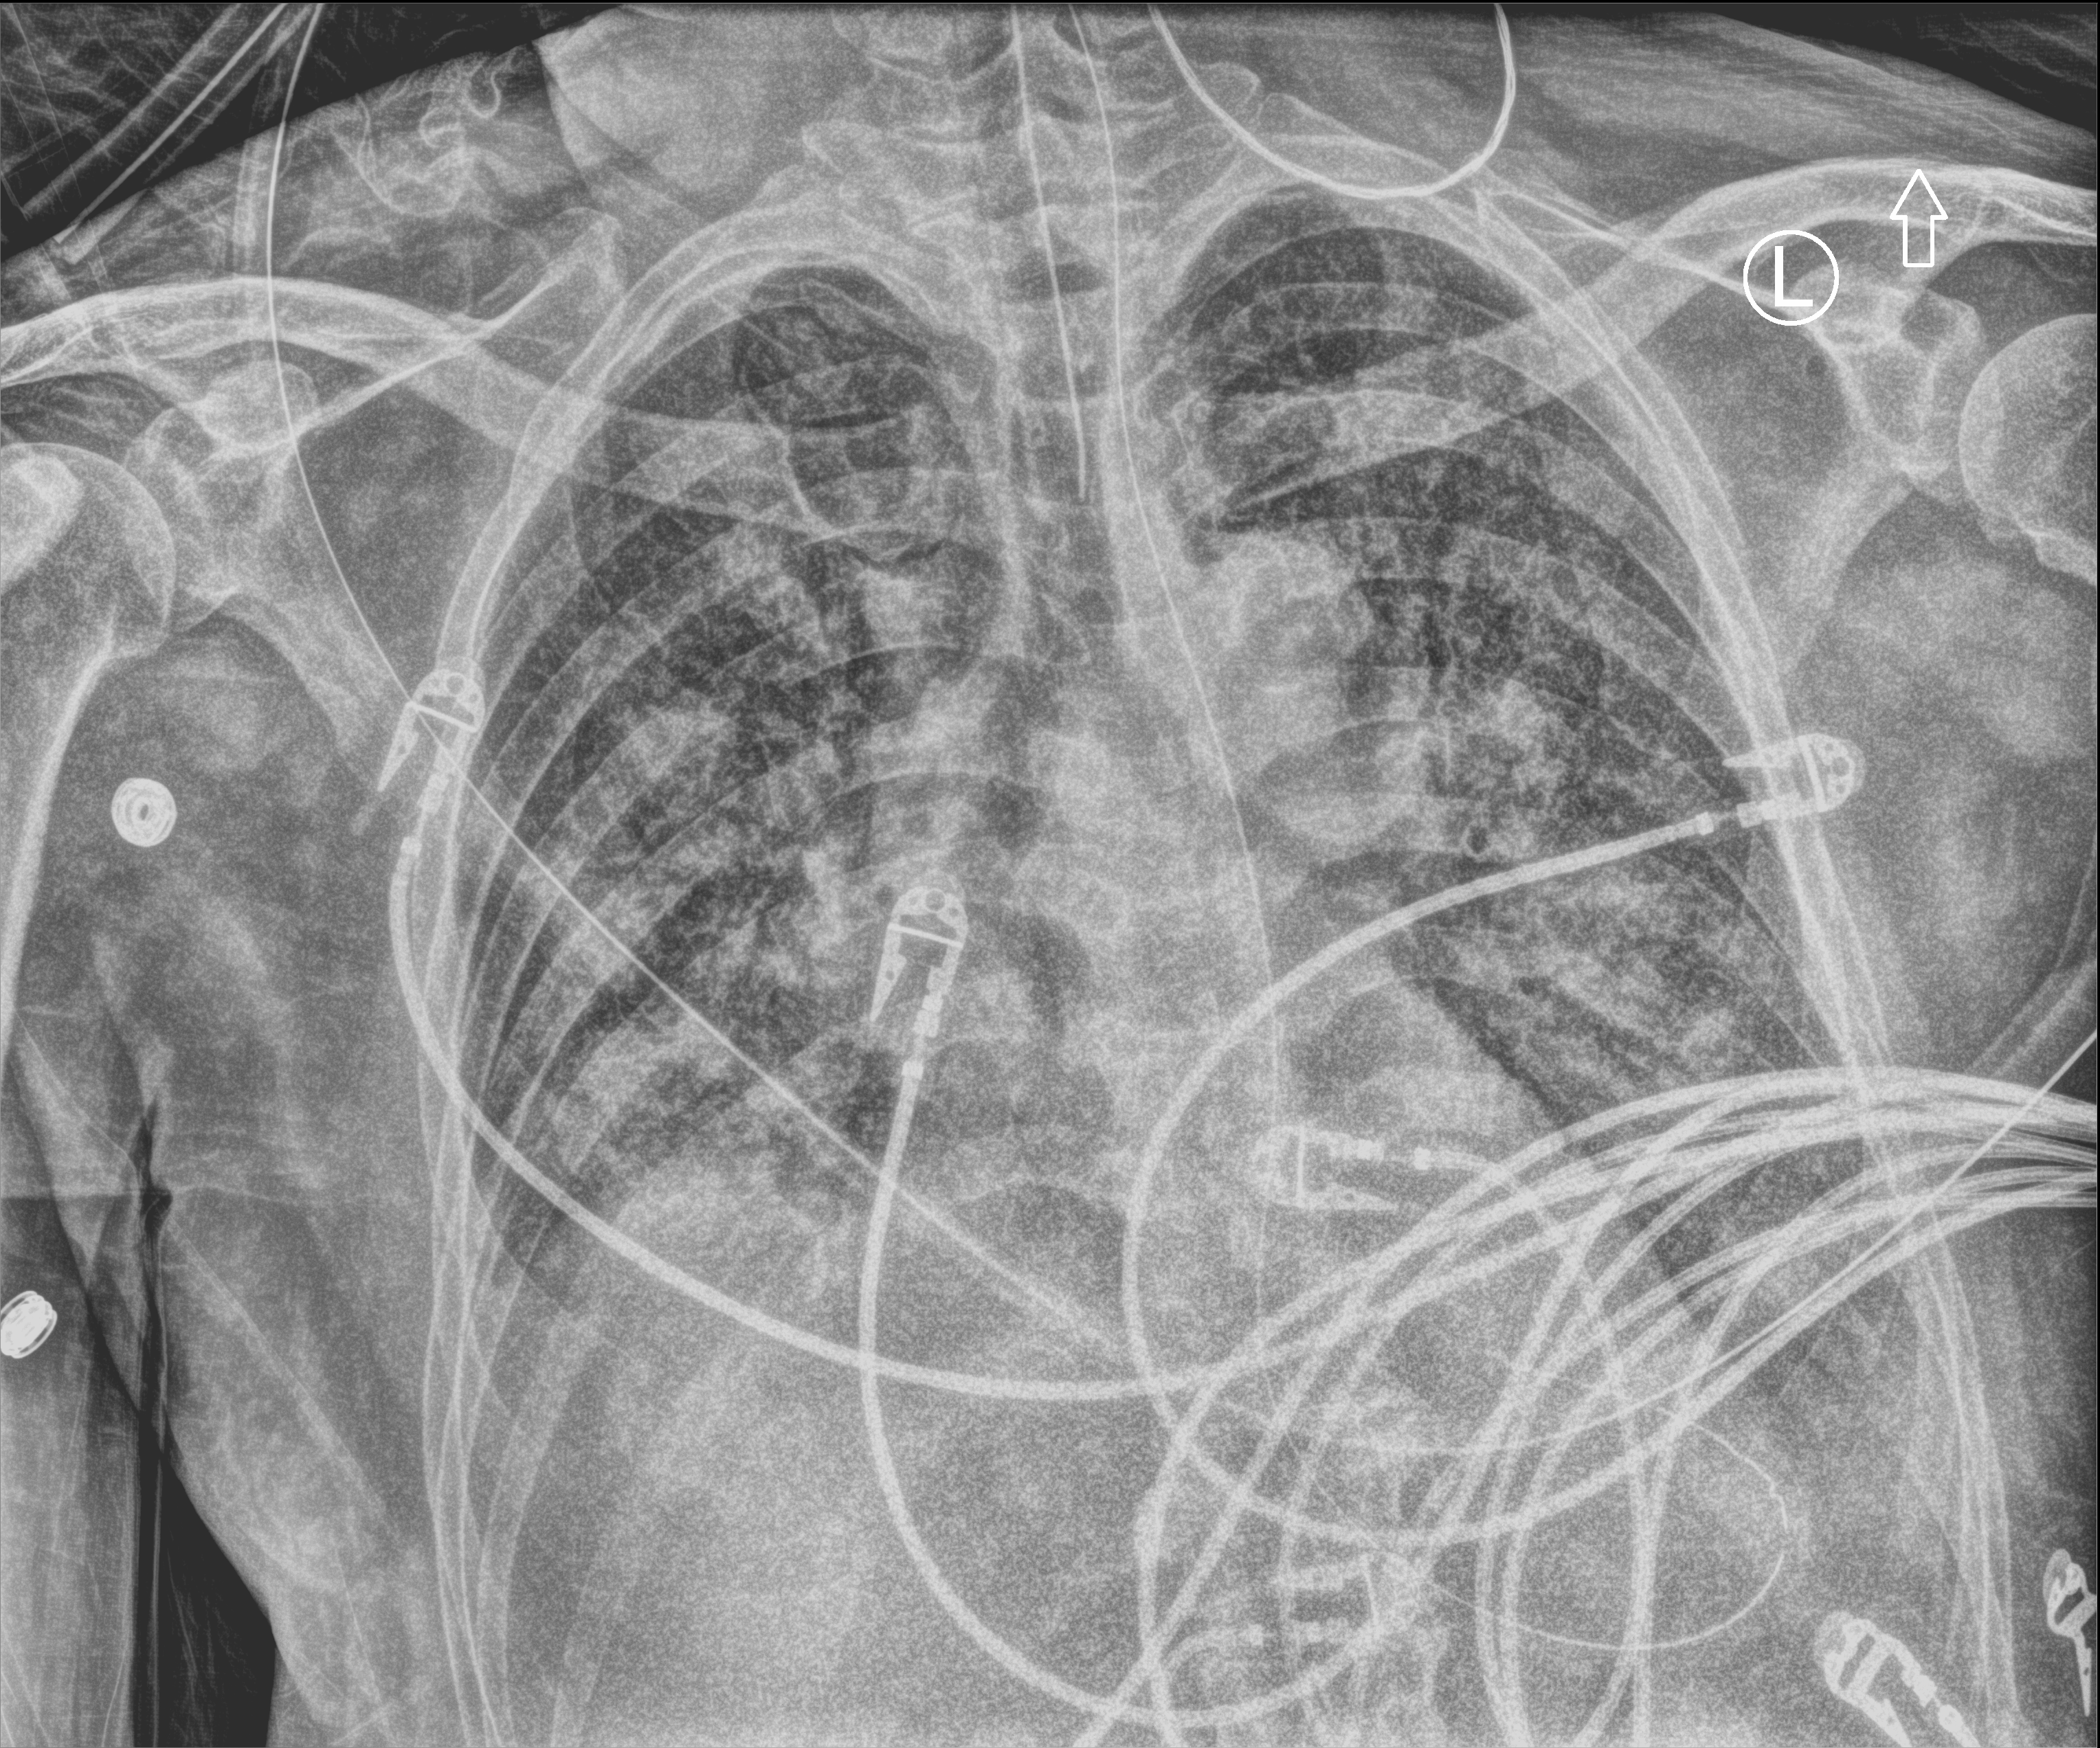
Bedside chest radiograph (computed radiography), anteroposterior (AP) projection. Patient hospitalised with COVID-19; male, aged 60–74 years.
From the hospital-stay record, not from the radiograph (when in the stay this image was taken is not recorded): COPD (admission record): no; length of hospital stay: 14 days.